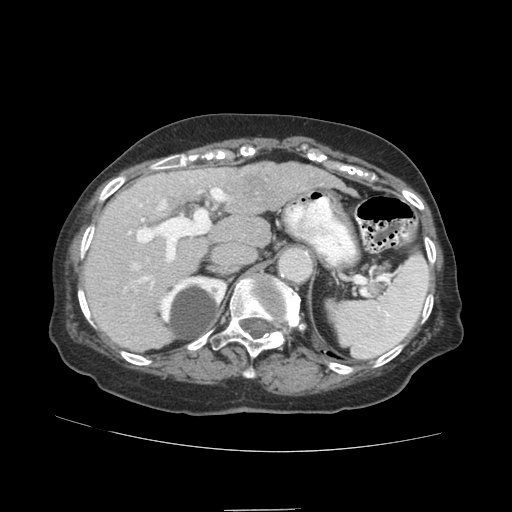
Contrast-enhanced abdominal CT (liver protocol), one axial slice. Position 58 of 89 along the scan axis. 140 kVp. Soft-tissue window (W 400 / L 40 HU). 2.5 mm slice thickness. 512 × 512 image matrix, field of view 360 × 360 mm. Case-level facts recorded for this patient, not image findings: diagnosis: hepatocellular carcinoma (patient treated with transarterial chemoembolisation; whether this scan precedes or follows treatment is not stated here); TNM stage (as recorded): Stage-II; Child-Pugh class: A; tumour differentiation: moderately differentiated.
Outlined on this slice (semi-automatic segmentation, software-assisted and operator-edited):
- liver parenchyma outside the tumour (the mass and vessels are separate outlines, so this box may not span the whole liver): bounding box [x1, y1, x2, y2] px = [84, 162, 334, 350]
- mass: [227, 163, 293, 213]
- liver vessels: [92, 173, 230, 292]